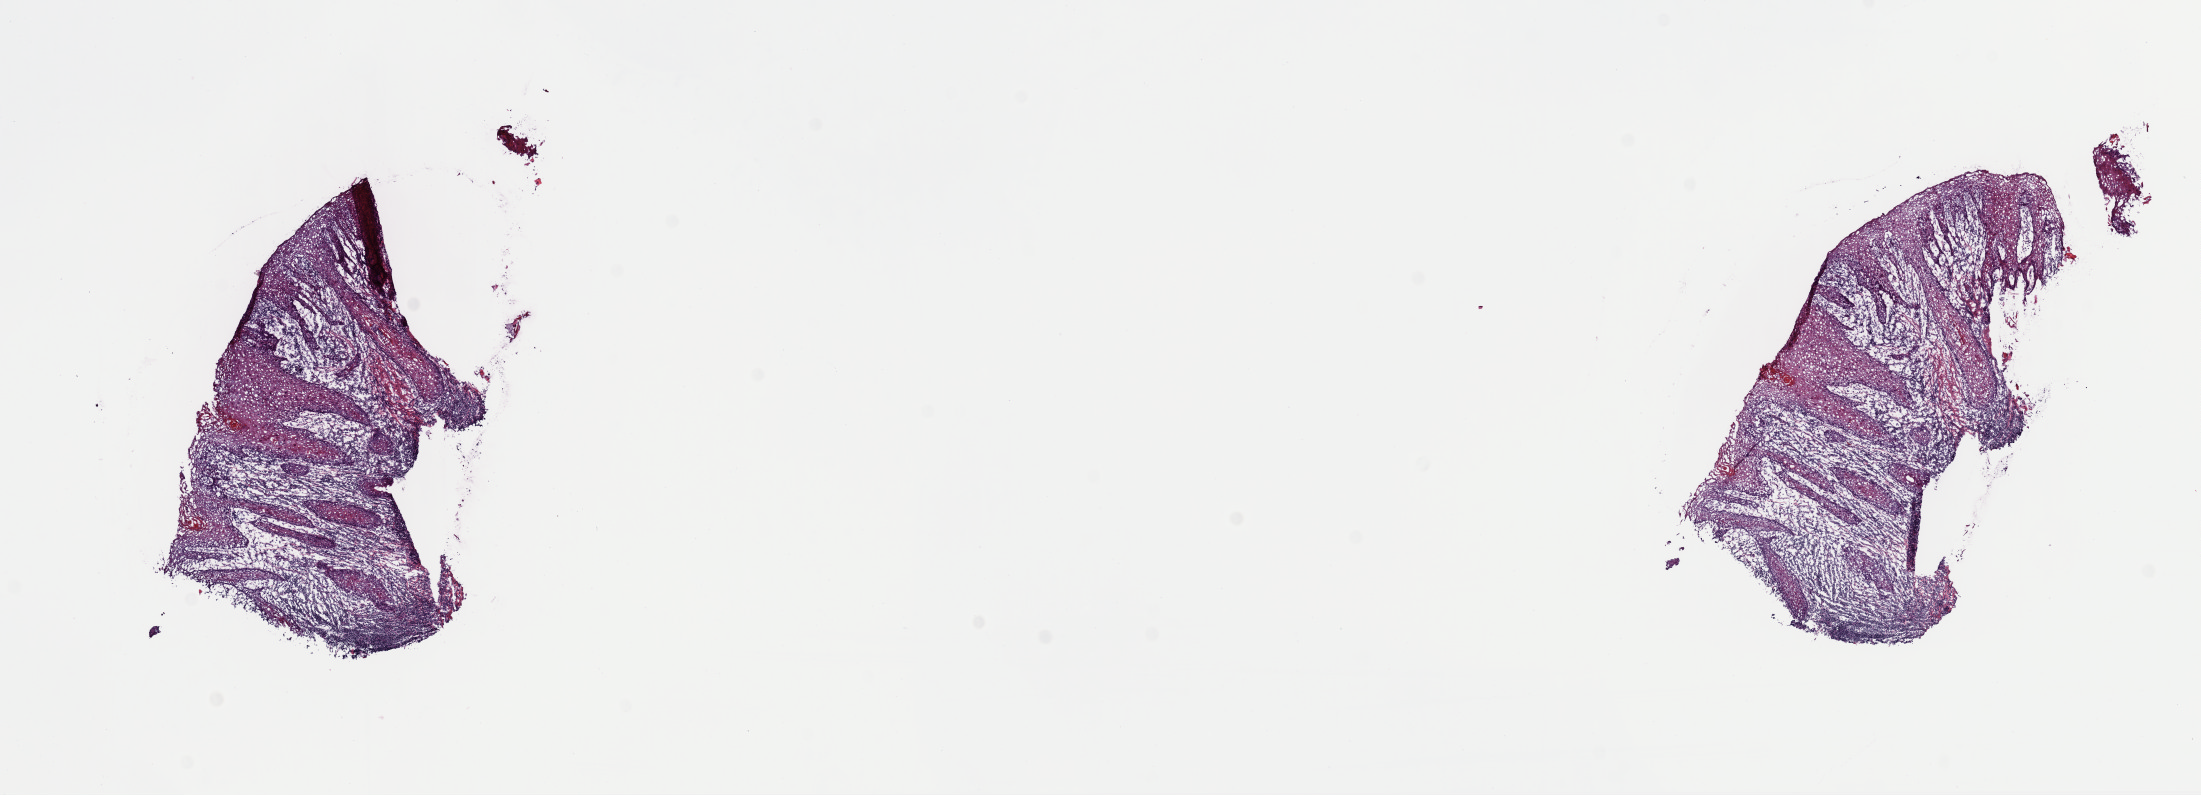
Digitized H&E-stained tissue section (whole slide), a low-resolution overview of the entire scanned area, about 17.4 x 6.3 mm; frozen section from the top of the tissue portion; sample: primary tumour, head and neck. Female, age 76 years at initial diagnosis. Histologic grade: G2 (moderately differentiated). Composition of this section per pathologist review: tumour cells 35%, tumour nuclei 65%, normal cells 0%, stromal cells 60%, necrosis 5%. Infiltration values recorded for this section: lymphocyte infiltration 15%, monocyte infiltration 2%, neutrophil infiltration 2%.
- AJCC pathologic stage: II (7th edition)
- laterality: right
- diagnosis: Squamous cell carcinoma, keratinizing, NOS (tongue, NOS)